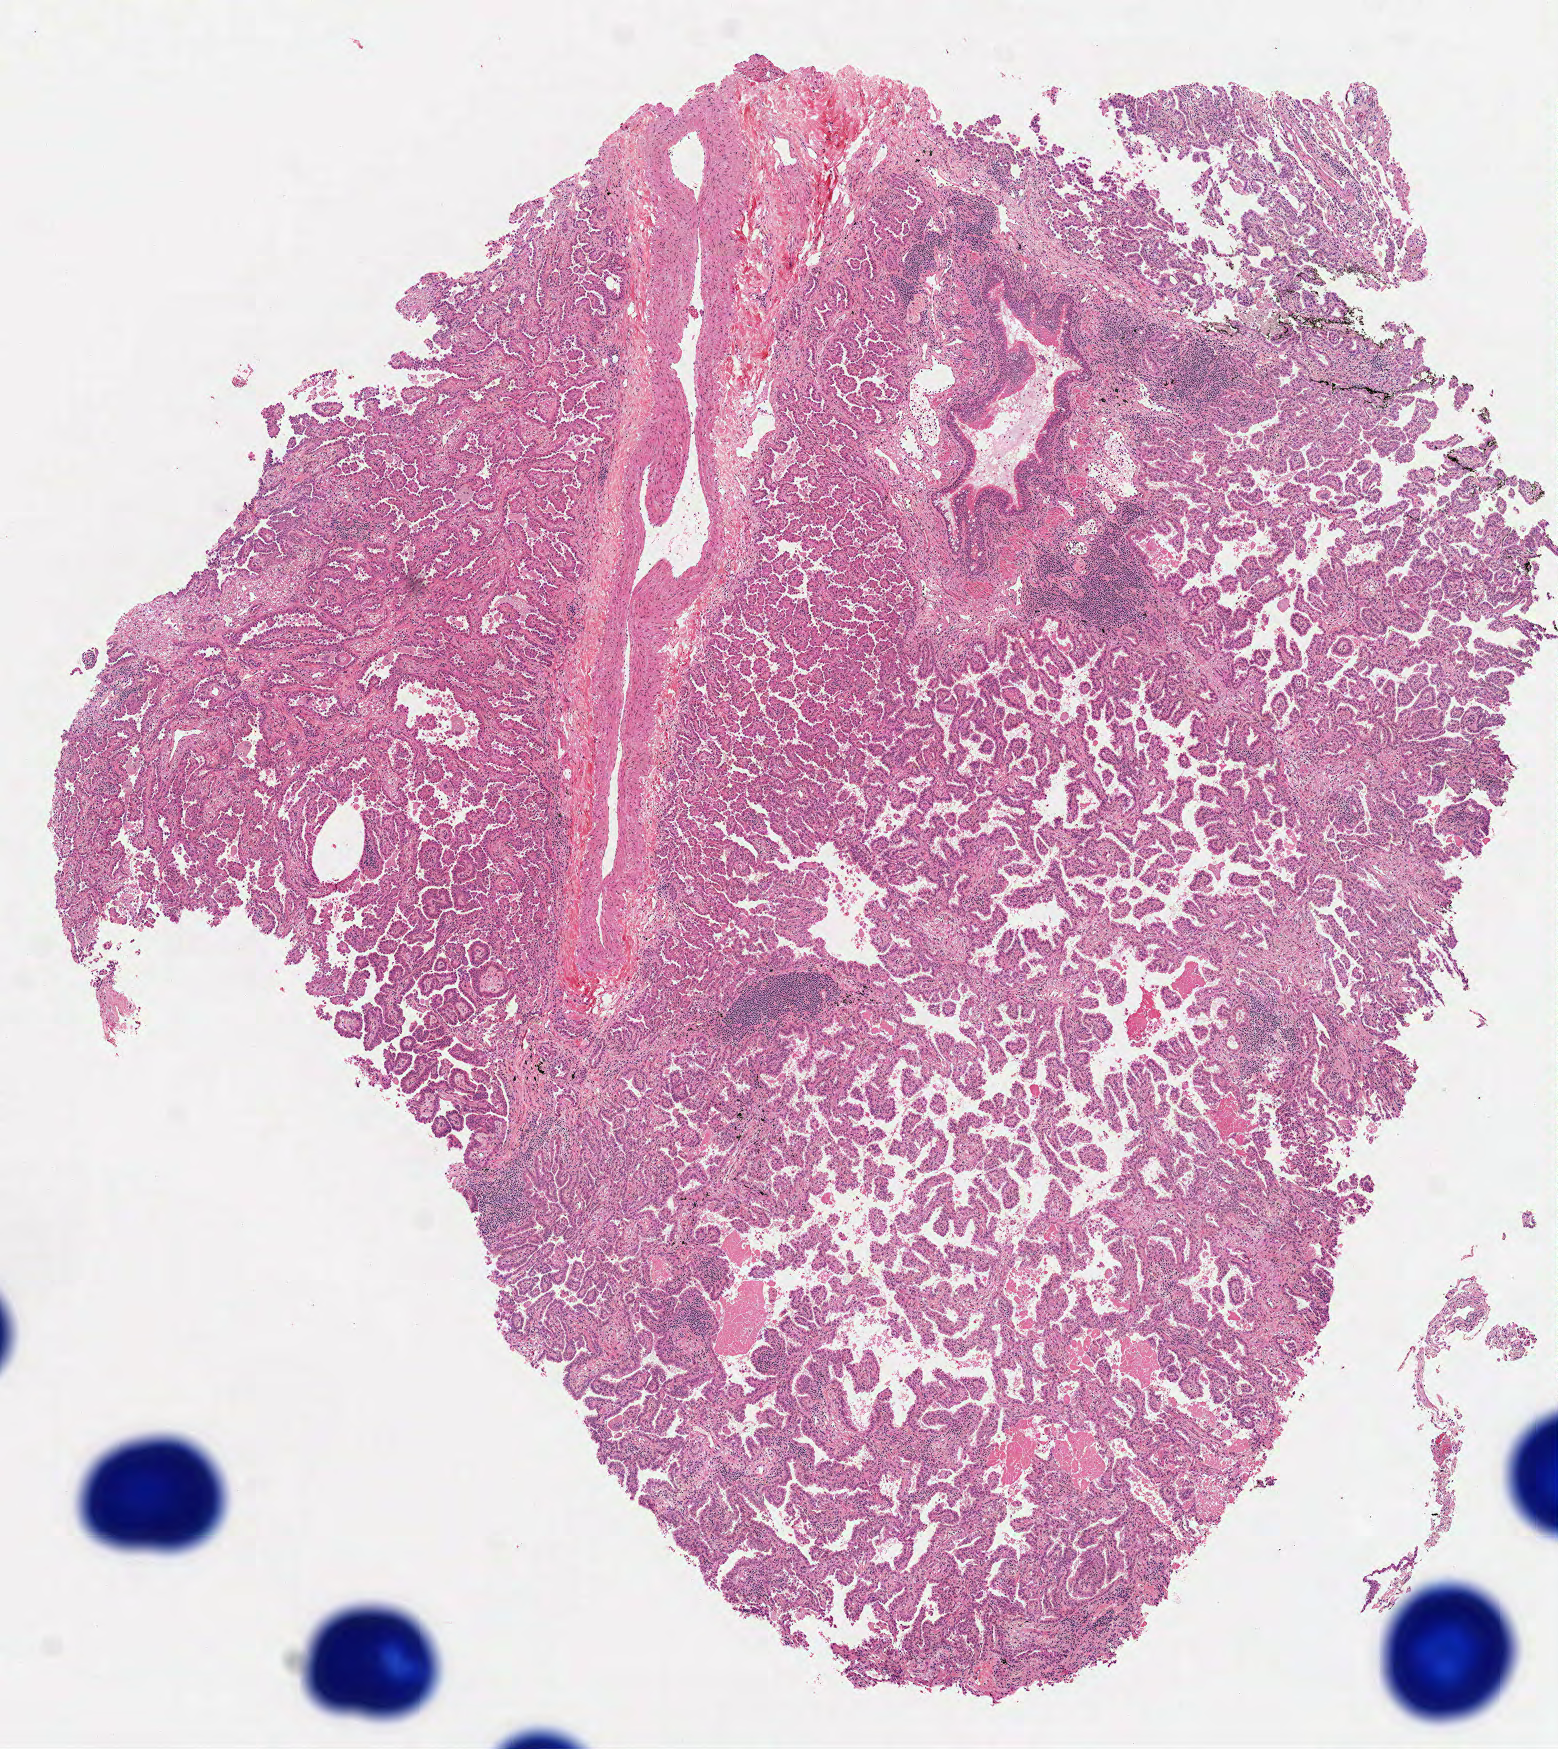
Whole-slide histology image, H&E-stained, whole scanned area (about 6.3 x 7.1 mm) shown as a low-resolution overview; frozen section from the top of the tissue portion; lung, primary tumour sample. Patient: male, age at initial diagnosis 72 years. Composition of this section per pathologist review: tumour cells 90%, tumour nuclei 80%, normal cells 10%, stromal cells 0%, necrosis 0%.
Histologic diagnosis: Adenocarcinoma with mixed subtypes (upper lobe, lung). AJCC pathologic stage: IB (6th edition). TNM: T2 N0 M0.